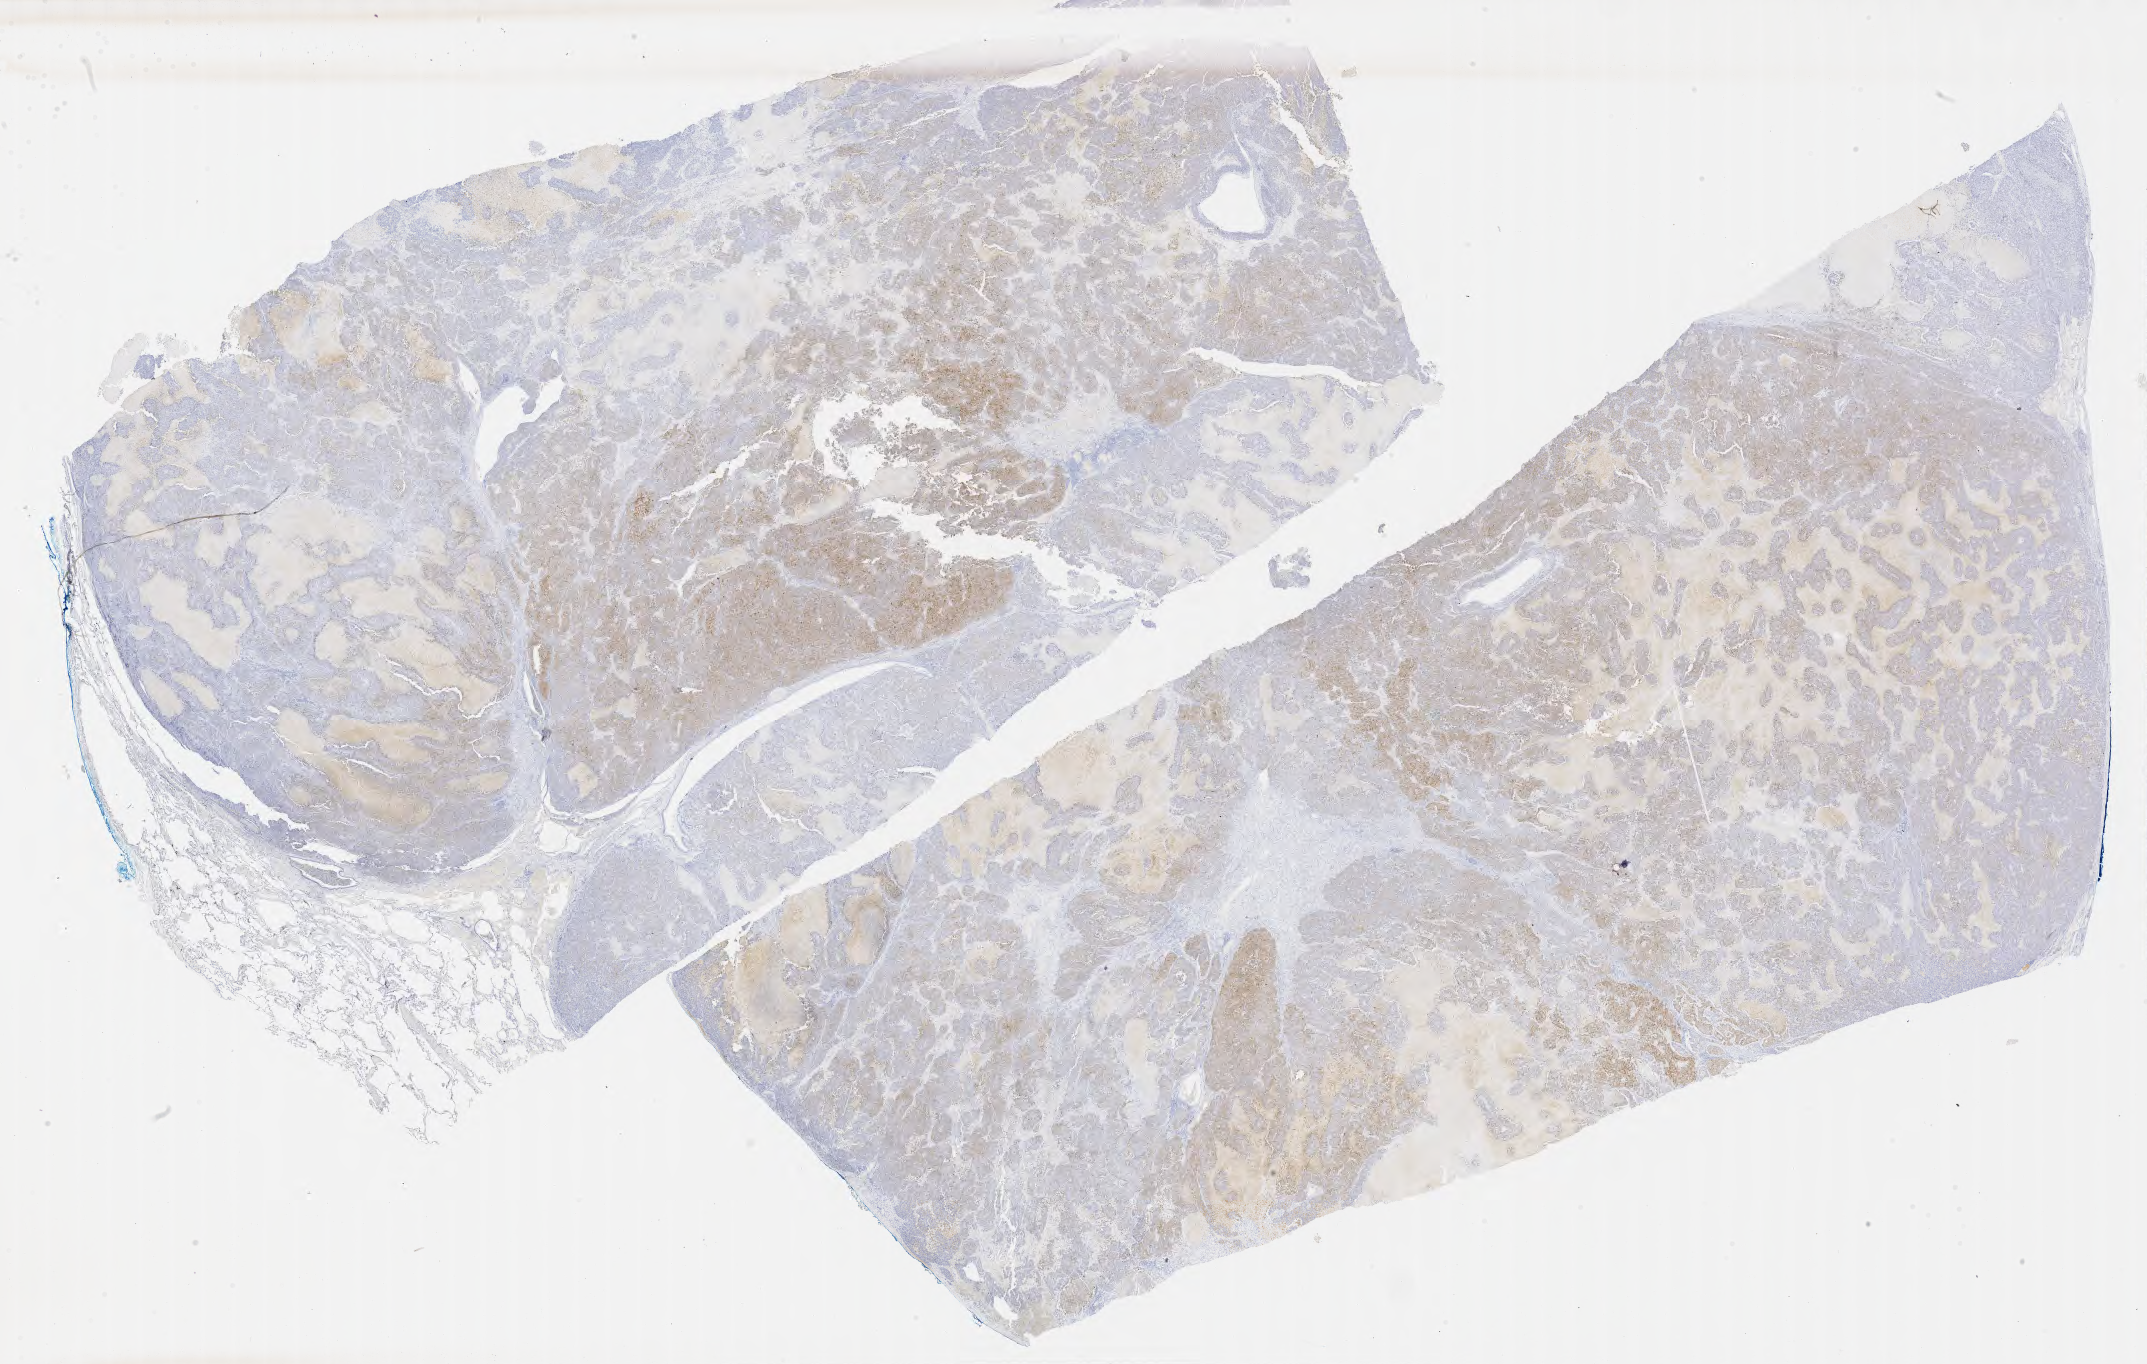
Whole-slide image, immunohistochemical stain for chromogranin, low-resolution overview of the scanned area, about 34.7 x 22.0 mm. Specimen: tumor tissue. Anatomic site: lung. Female patient, aged 61.
* histologic diagnosis: Large cell neuroendocrine carcinoma